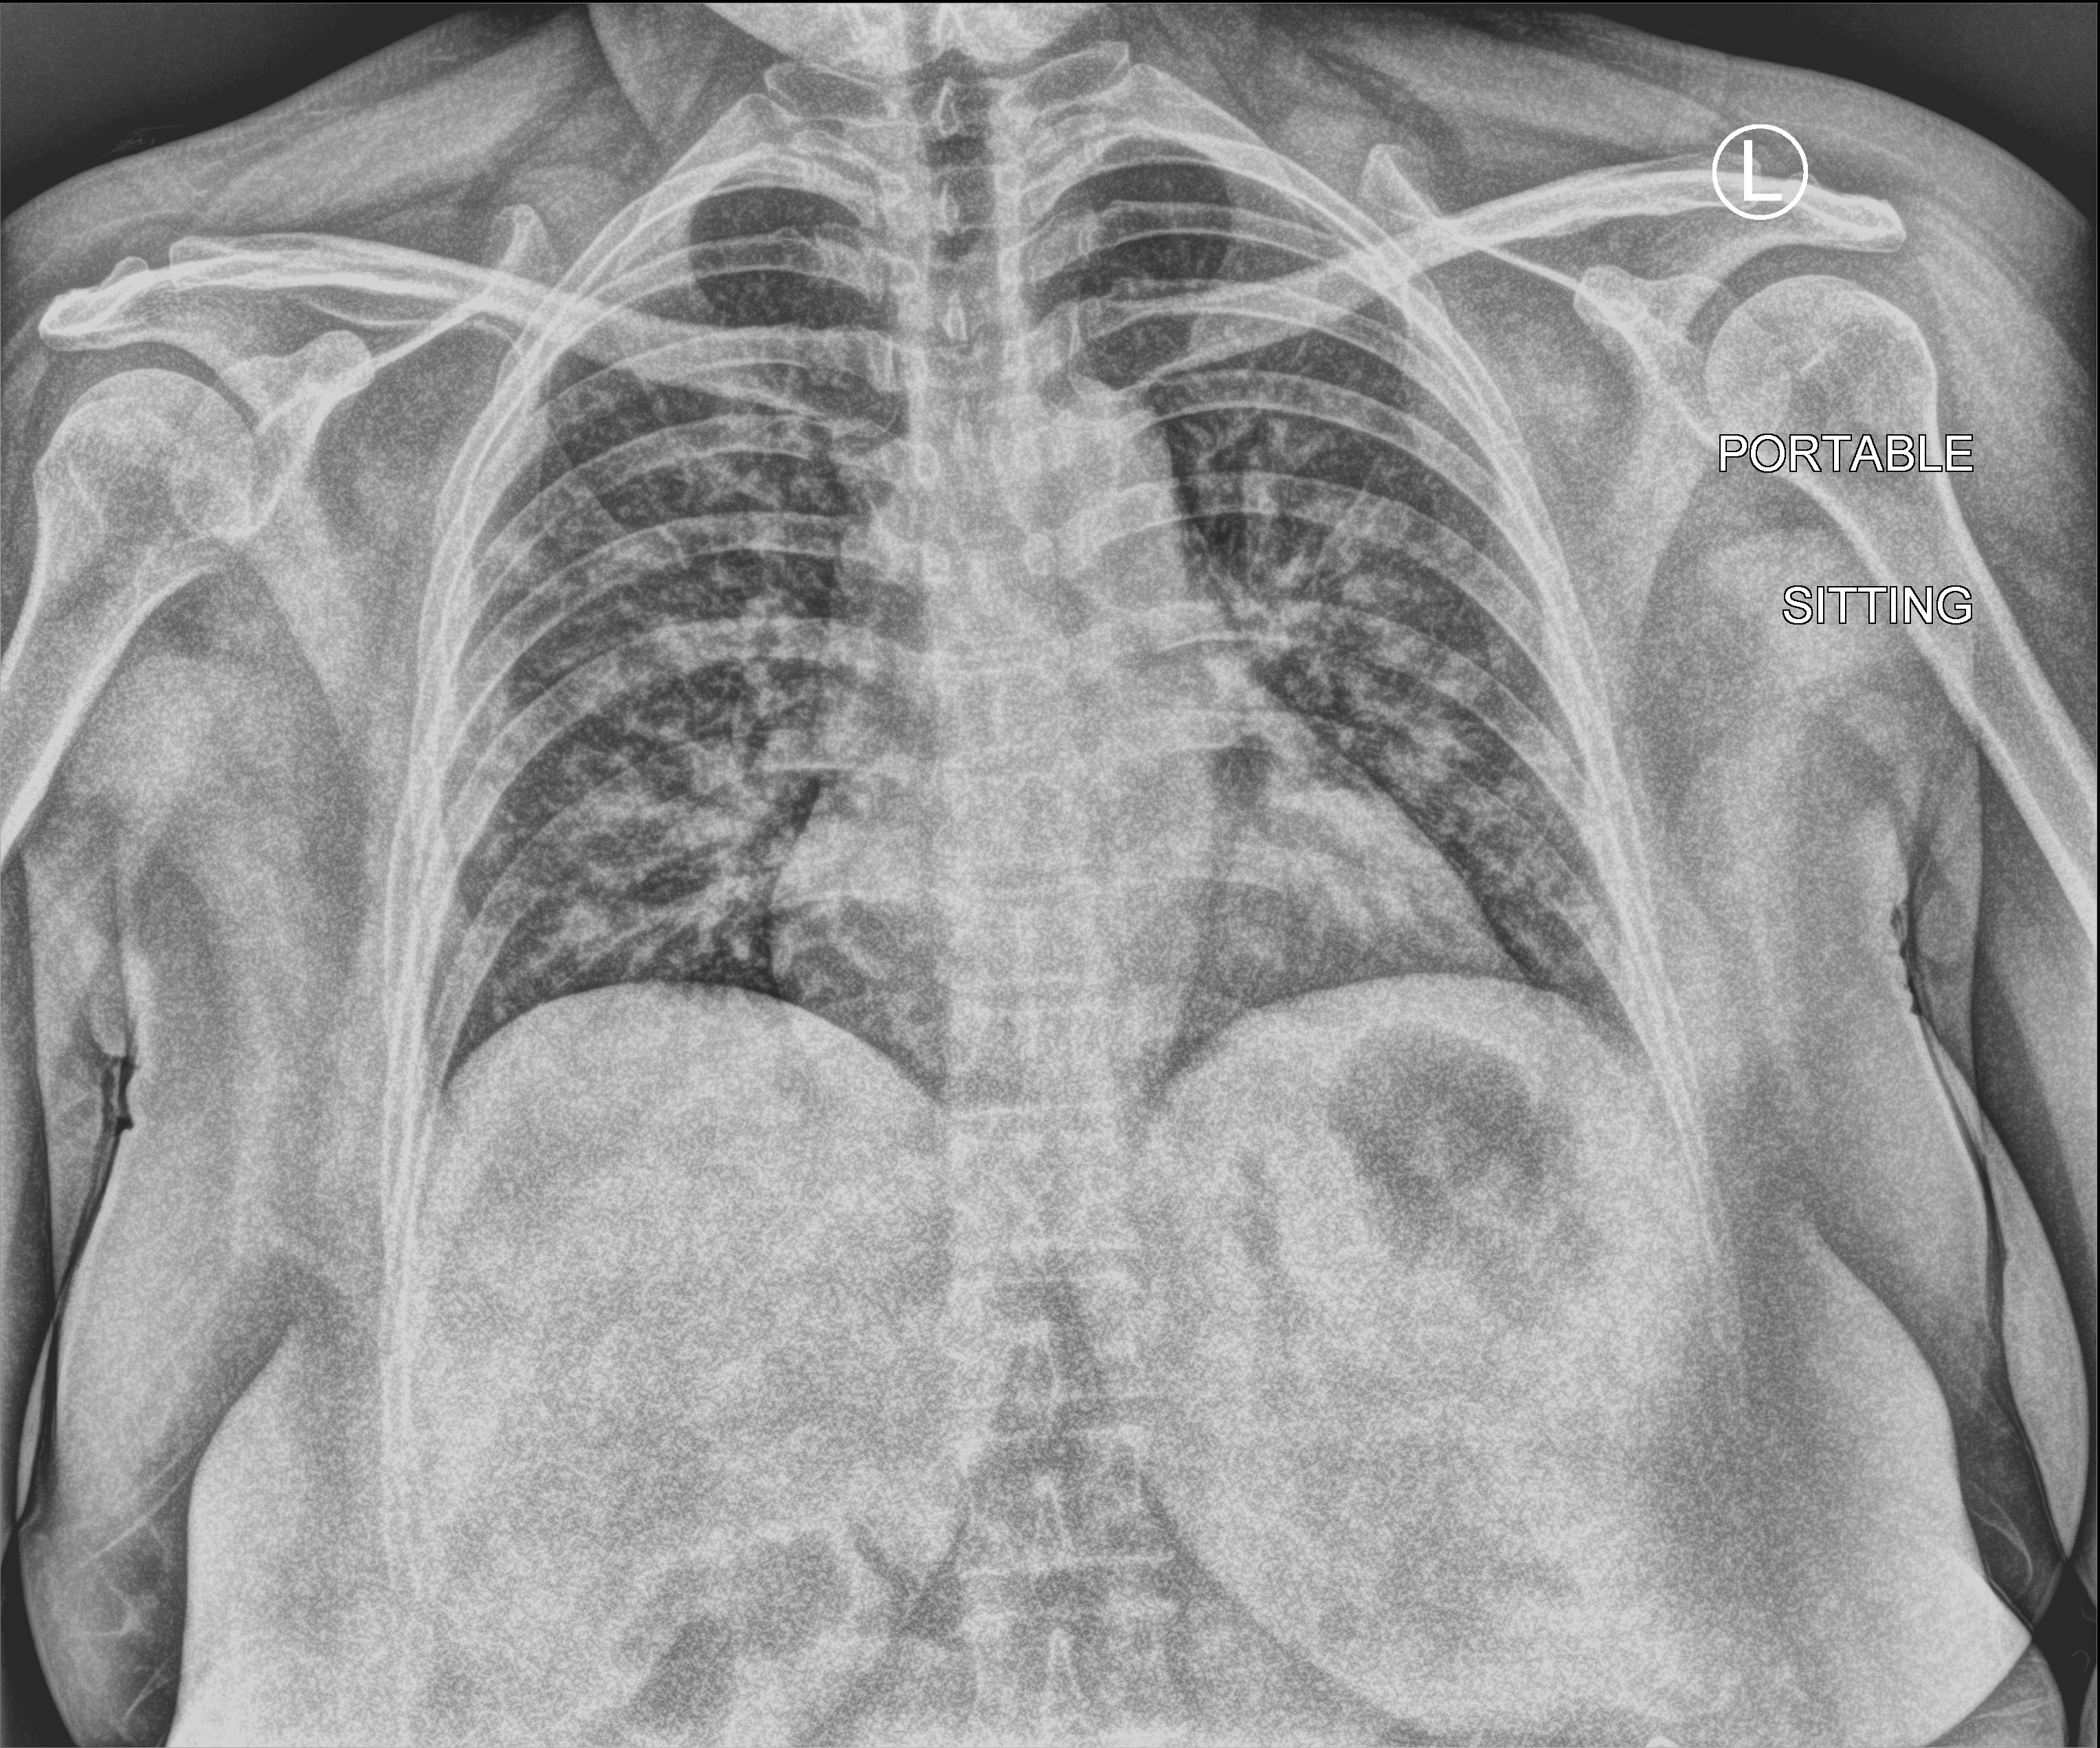
Portable chest radiograph; anteroposterior (AP) projection. Patient hospitalised with COVID-19; female, aged 18–59 years.
From the hospital-stay record, not from the radiograph (when in the stay this image was taken is not recorded): diabetes (admission record): no.